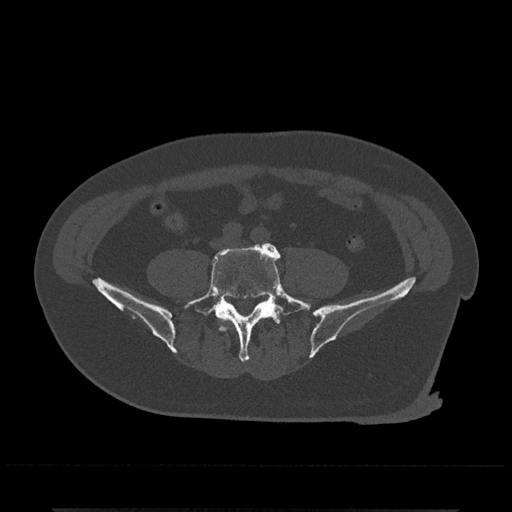
CT including the spine, one axial slice. Position 90 of 797 along the scan axis. Bone window (W 1800 / L 400 HU). 512 × 512 image matrix. Male patient, age 67 years. From the clinical record (not read from this slice): primary cancer: prostate.
Annotated regions visible in this slice (semi-automatically segmented with operator editing):
- L4 vertebra: bounding box <221,327,227,331> (left, top, right, bottom; pixels)
- L5 vertebra: <184,242,311,363>